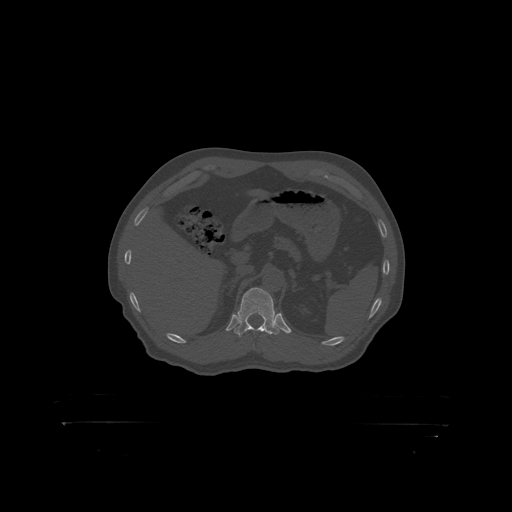
CT including the spine, one axial slice; slice 356 of 399 in the series (ordered by position); 120 kVp; bone window (W 1800 / L 400 HU); 512 × 512 image matrix. Male patient, age 46 years. Case-level facts recorded for this patient, not image findings: primary cancer: skin.
Annotated regions visible in this slice (semi-automatically segmented with operator editing):
- T12 vertebra: bounding box <234,288,280,319> (left, top, right, bottom; pixels)